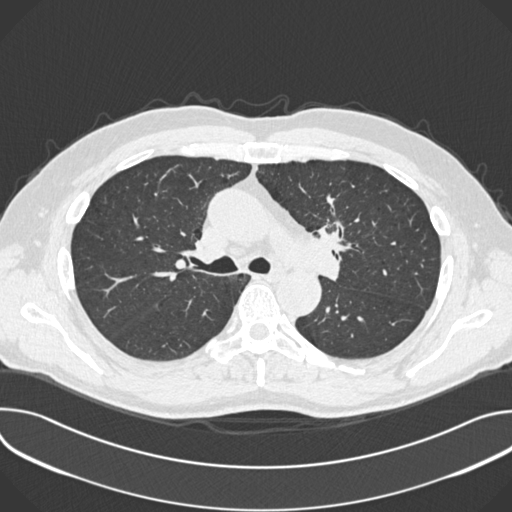
Low-dose screening chest CT, one axial slice; slice 244 of 361 in the series (ordered by position); reconstruction kernel B30f; 120 kVp; lung window (W 1500 / L -600 HU); 1 mm slice thickness; 512 × 512 image matrix.
Annotated regions visible in this slice (manually delineated by an expert):
- lesion 1 (tumor, upper lobe of left lung): bounding box <318,222,343,249> (left, top, right, bottom; pixels)